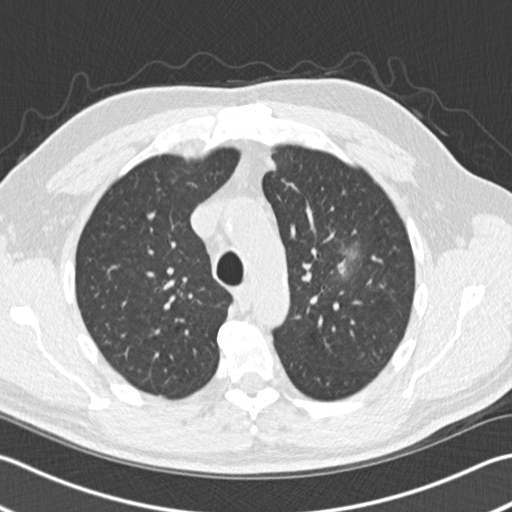
Low-dose screening chest CT, one axial slice. Position 114 of 153 along the scan axis. Reconstruction kernel B30f. 120 kVp. Lung window (W 1500 / L -600 HU). 2 mm slice thickness. 512 × 512 image matrix, field of view 346 × 346 mm.
Annotated regions visible in this slice (expert manual segmentation):
- lesion 1 (tumor, upper lobe of left lung): bounding box [x1, y1, x2, y2] px = [339, 262, 346, 272]